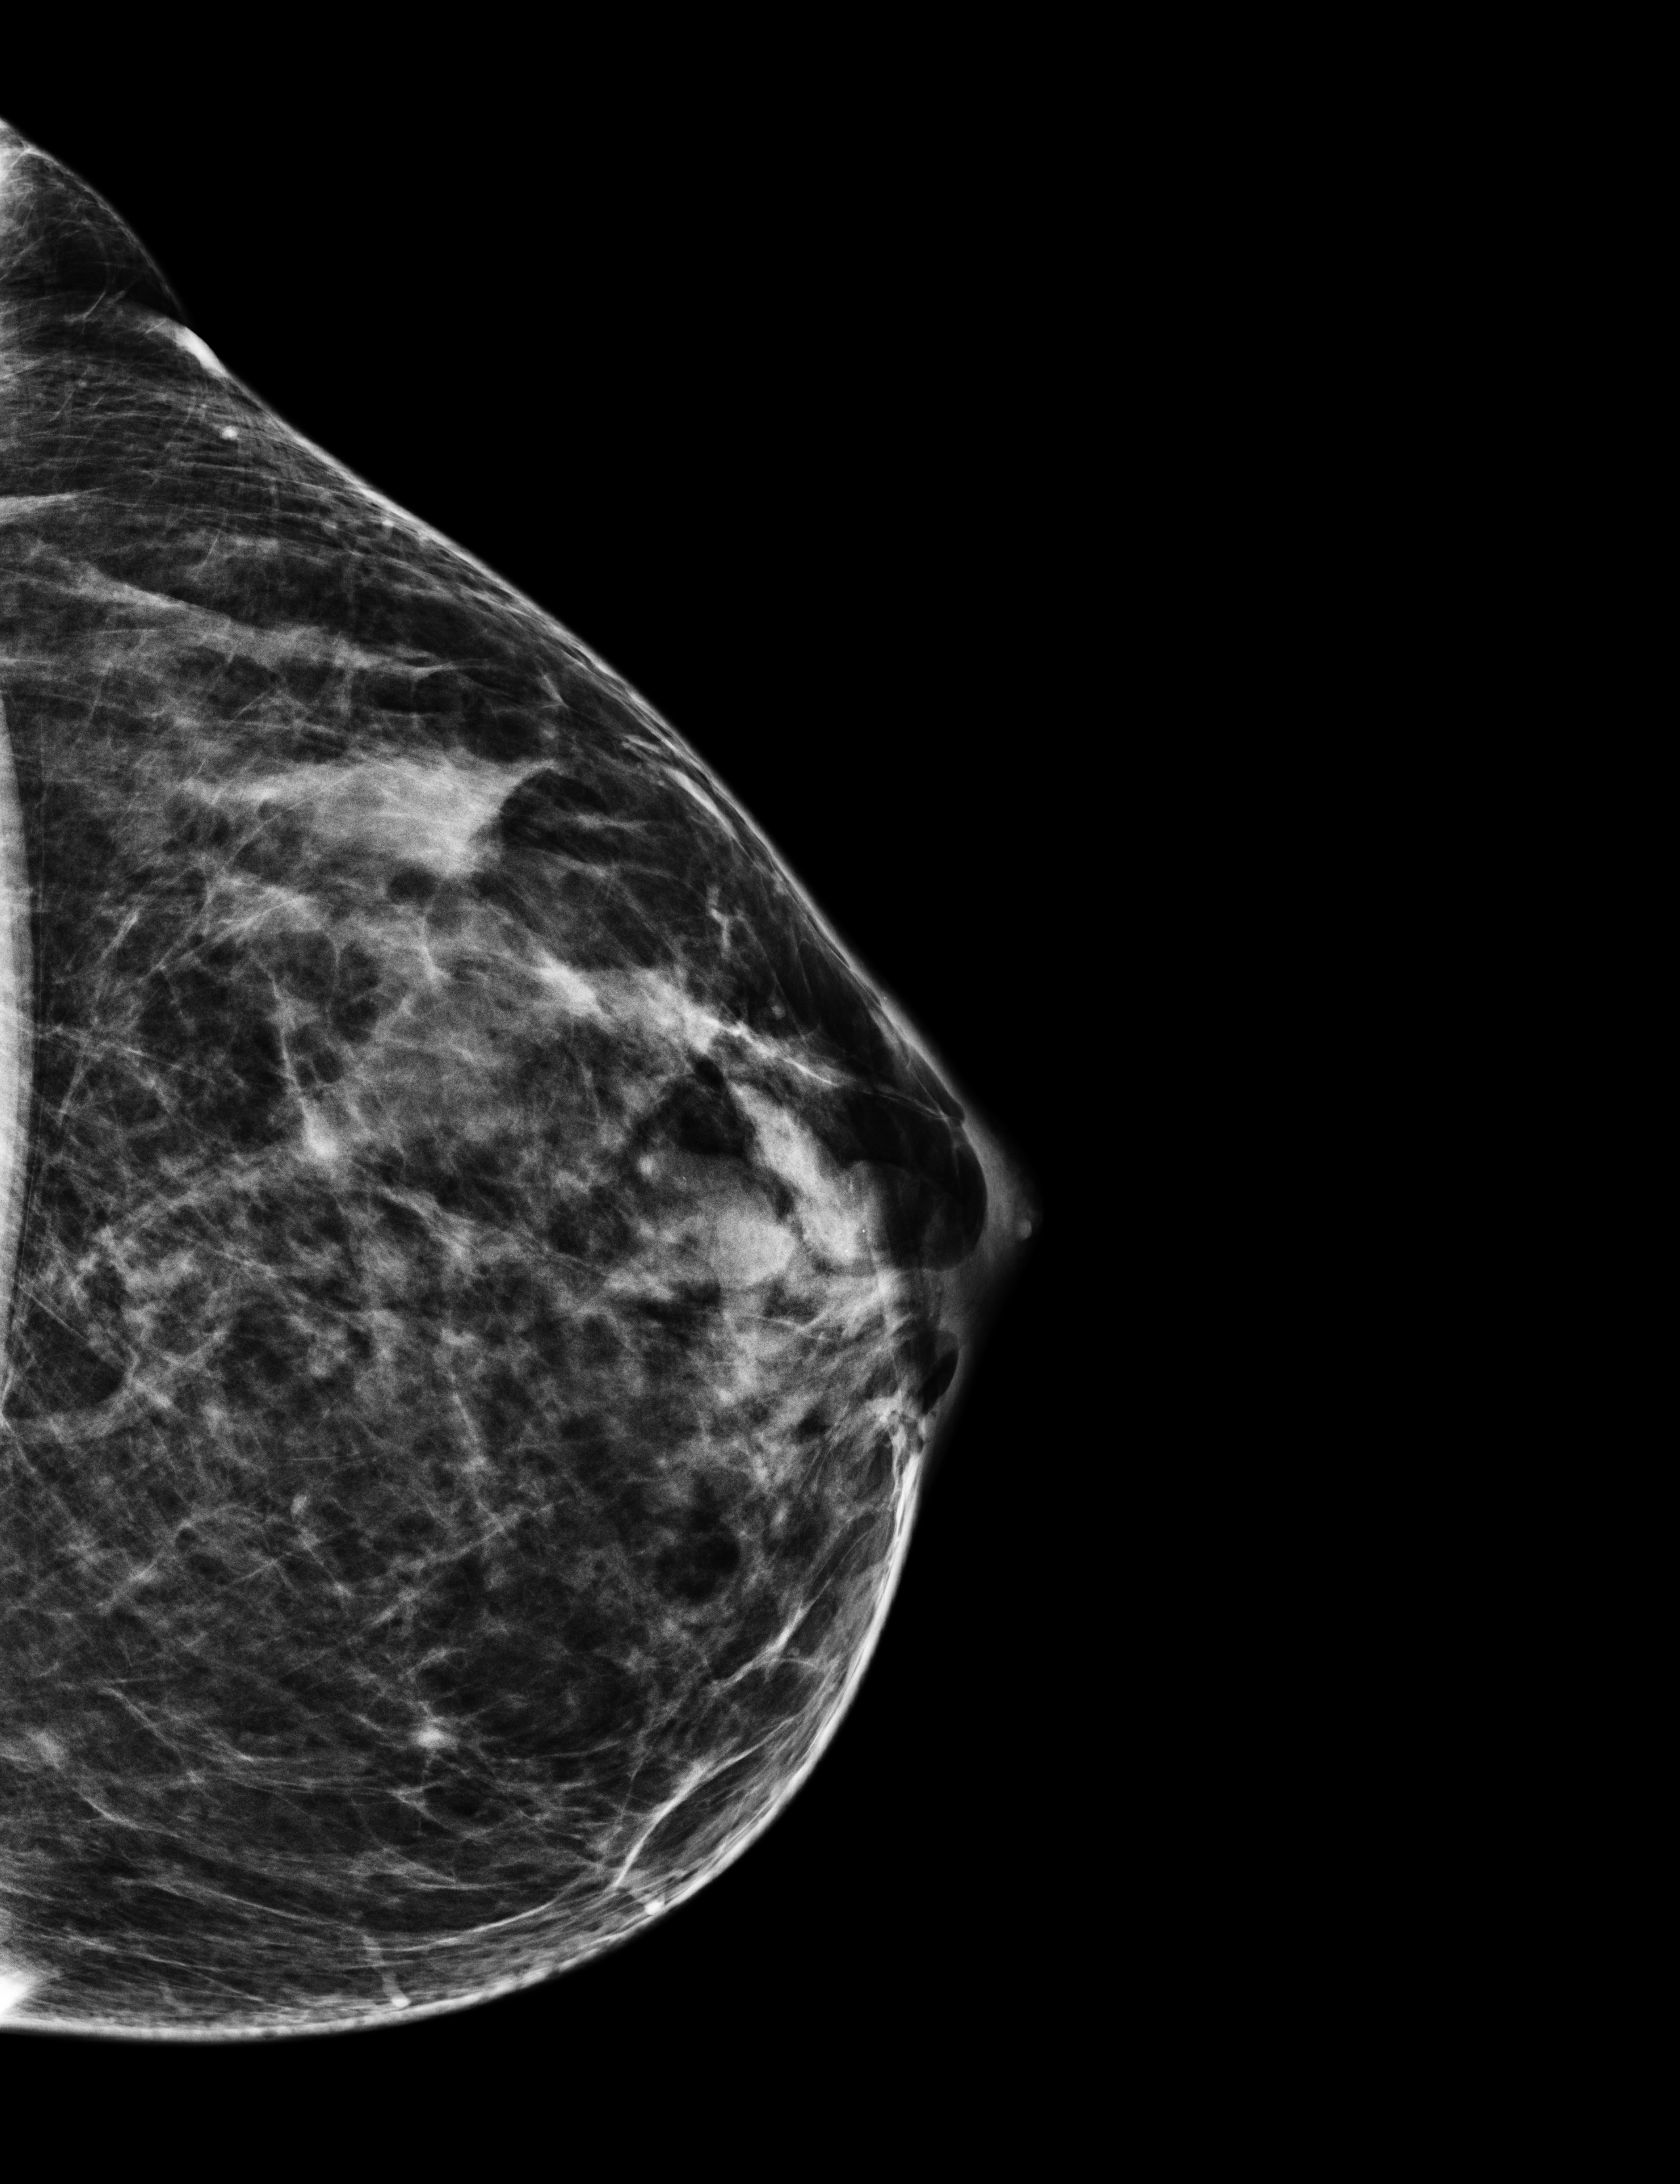
Annual screening mammography examination, compressed breast thickness 61 mm, system: Selenia Dimensions. Patient: female, 45 years.
Image type: full-field digital mammogram. Breast: left. Projection: cranio-caudal projection.